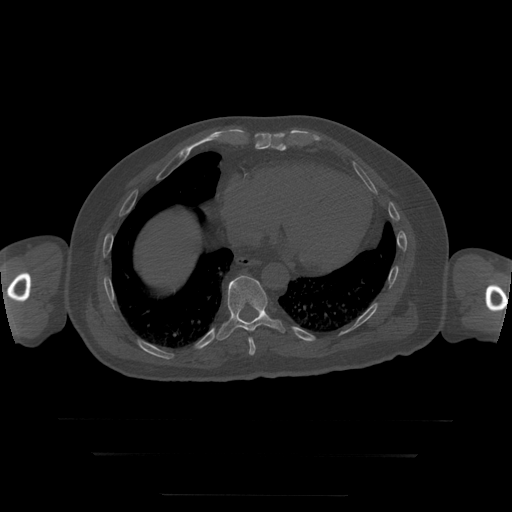
CT including the spine, one axial slice. Slice 126 of 397 in the series (ordered by position). 120 kVp. Bone window (W 1800 / L 400 HU). 1.25 mm slice thickness. 512 × 512 image matrix. Patient age 73 years. From the clinical record (not read from this slice): primary cancer: prostate.
Annotated regions visible in this slice (semi-automatic segmentation, software-assisted and operator-edited):
- T10 vertebra: bounding box [x1, y1, x2, y2] px = [217, 276, 286, 341]
- T9 vertebra: [249, 338, 256, 356]